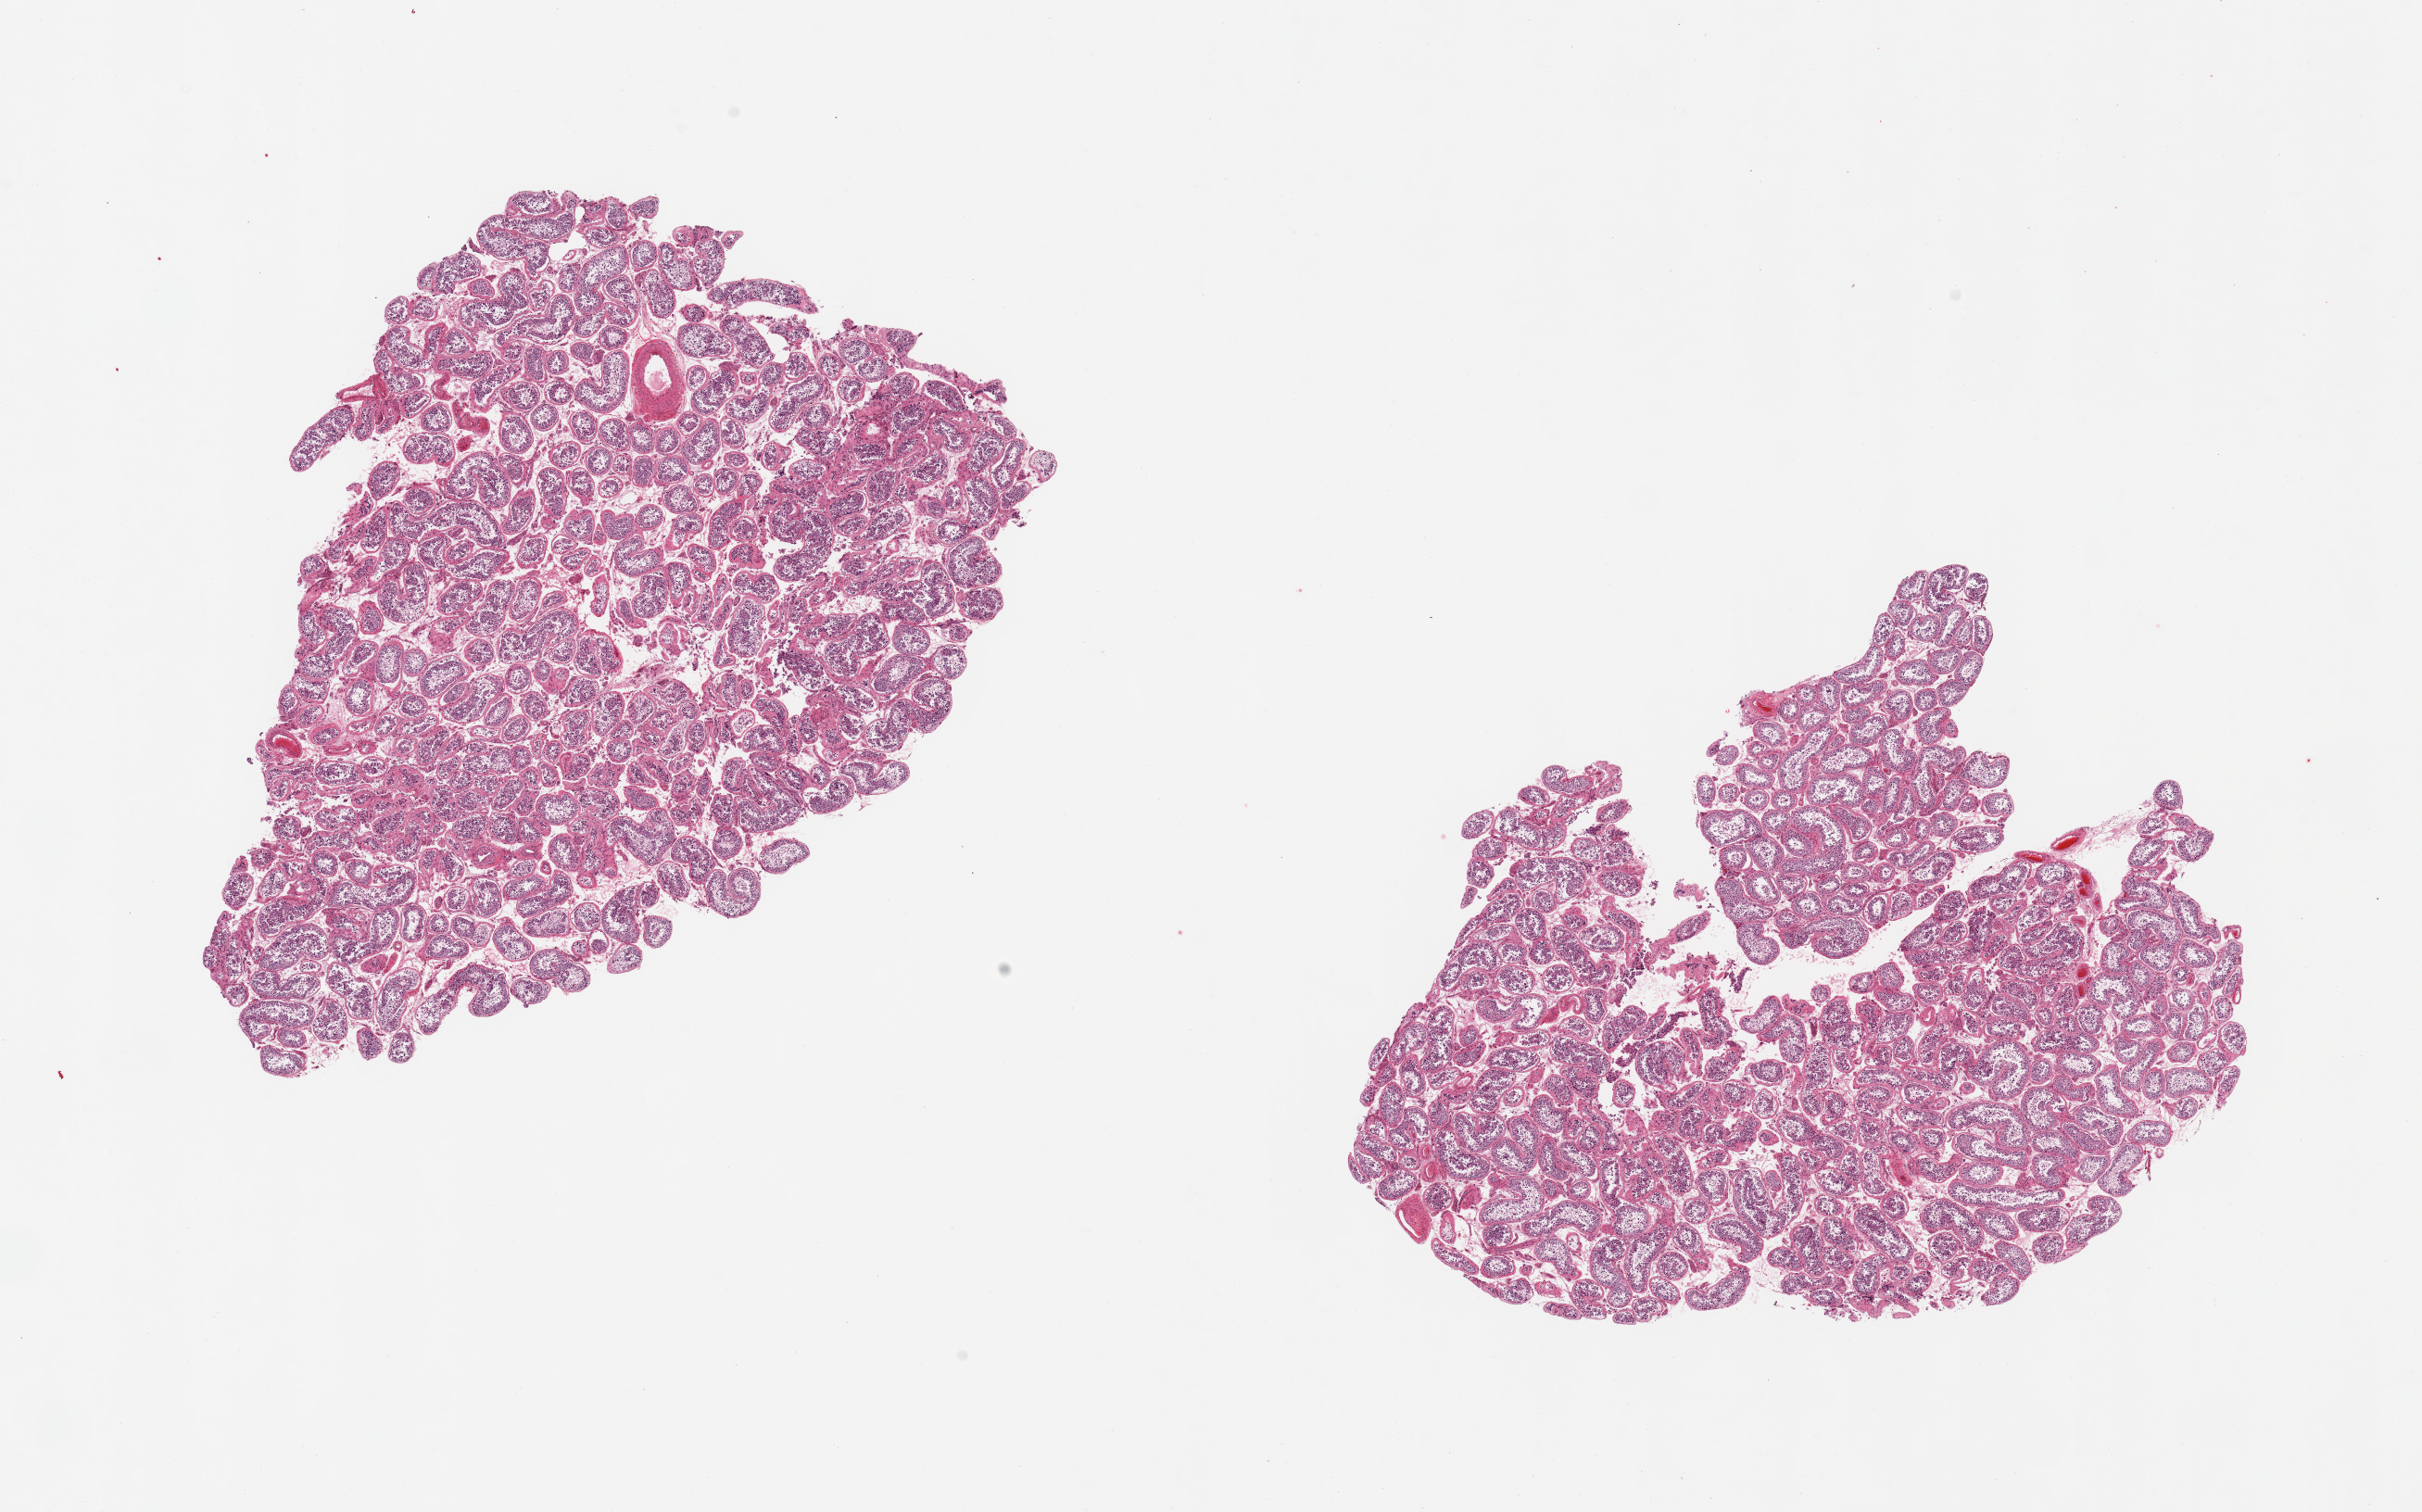
Digitized hematoxylin and eosin (H&E)-stained section, brightfield — low-resolution overview of the scanned area, about 20.7 x 12.9 mm (acquisition: 20x scan); PAXgene-fixed paraffin-embedded (PFPE) section; section of testis (target tissue); donor tissue sample.
- pathologist's review note for this sample: 2 aliquots, ~8x5mm. Spermatogenesis is noted